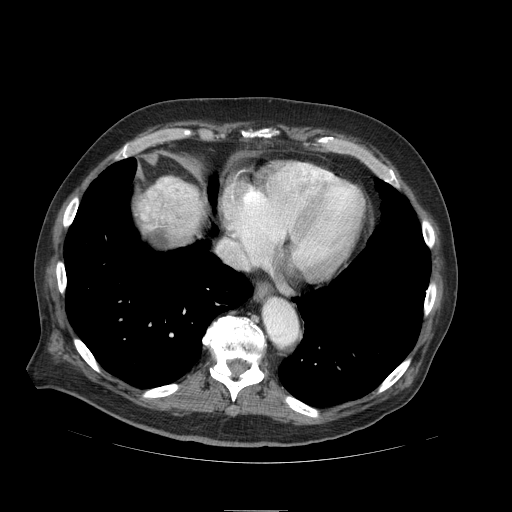
Contrast-enhanced abdominal CT (liver protocol), one axial slice; slice 85 of 103 in the series (ordered by position); reconstruction kernel STANDARD; 120 kVp; soft-tissue window (W 400 / L 40 HU); 512 × 512 image matrix. Case-level facts recorded for this patient, not image findings: diagnosis: hepatocellular carcinoma (patient treated with transarterial chemoembolisation; whether this scan precedes or follows treatment is not stated here); TNM stage (as recorded): Stage-IIIA; Child-Pugh class: B; tumour differentiation: well differentiated; tumour nodularity: multinodular.
Annotated regions visible in this slice (semi-automatic segmentation, software-assisted and operator-edited):
- liver parenchyma outside the tumour (the mass and vessels are separate outlines, so this box may not span the whole liver): bounding box (x1, y1, x2, y2) in pixels: (146, 176, 196, 244)
- mass: (133, 176, 206, 244)